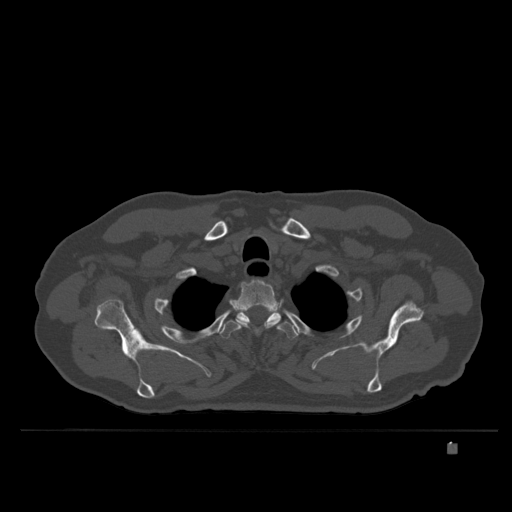
CT including the spine, one axial slice. Slice 307 of 435 in the series (ordered by position). Bone window (W 1800 / L 400 HU). 1.5 mm slice thickness. 512 × 512 image matrix, field of view 434 × 434 mm. Patient: male, 73 years. Case-level facts recorded for this patient, not image findings: primary cancer: skin.
Annotated regions visible in this slice (semi-automatically segmented with operator editing):
- T2 vertebra: box from (x=230, y=280) to (x=281, y=335) px
- T3 vertebra: (x=219, y=308)–(x=299, y=340)